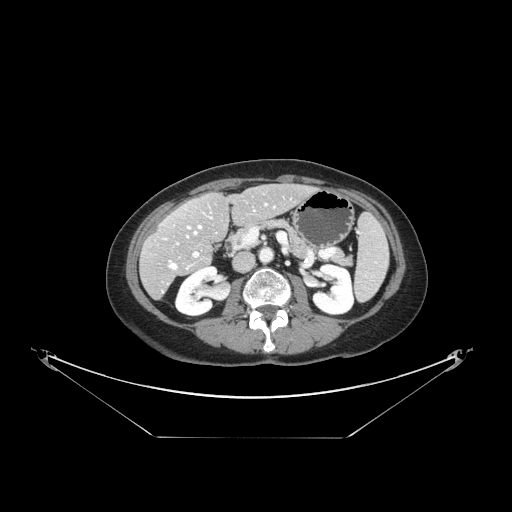
Contrast-enhanced abdominal CT, one axial slice; position 65 of 148 along the scan axis; 120 kVp; soft-tissue window (W 400 / L 40 HU); 2.5 mm slice thickness; 512 × 512 image matrix, field of view 500 × 500 mm. Female patient, age 73 years. Case-level facts recorded for this patient, not image findings: diagnosis: colorectal cancer liver metastases, imaged before liver resection; multiple liver metastases: no; largest metastasis: 1 cm; chemotherapy before resection: yes.
Outlined on this slice (manually delineated by an expert):
- hepatic veins: bounding box <169,216,212,269> (left, top, right, bottom; pixels)
- liver: <142,185,313,298>
- planned liver remnant (the part of the liver to remain after resection): <167,185,312,249>
- portal vein (with intrahepatic branches): <194,252,198,256>